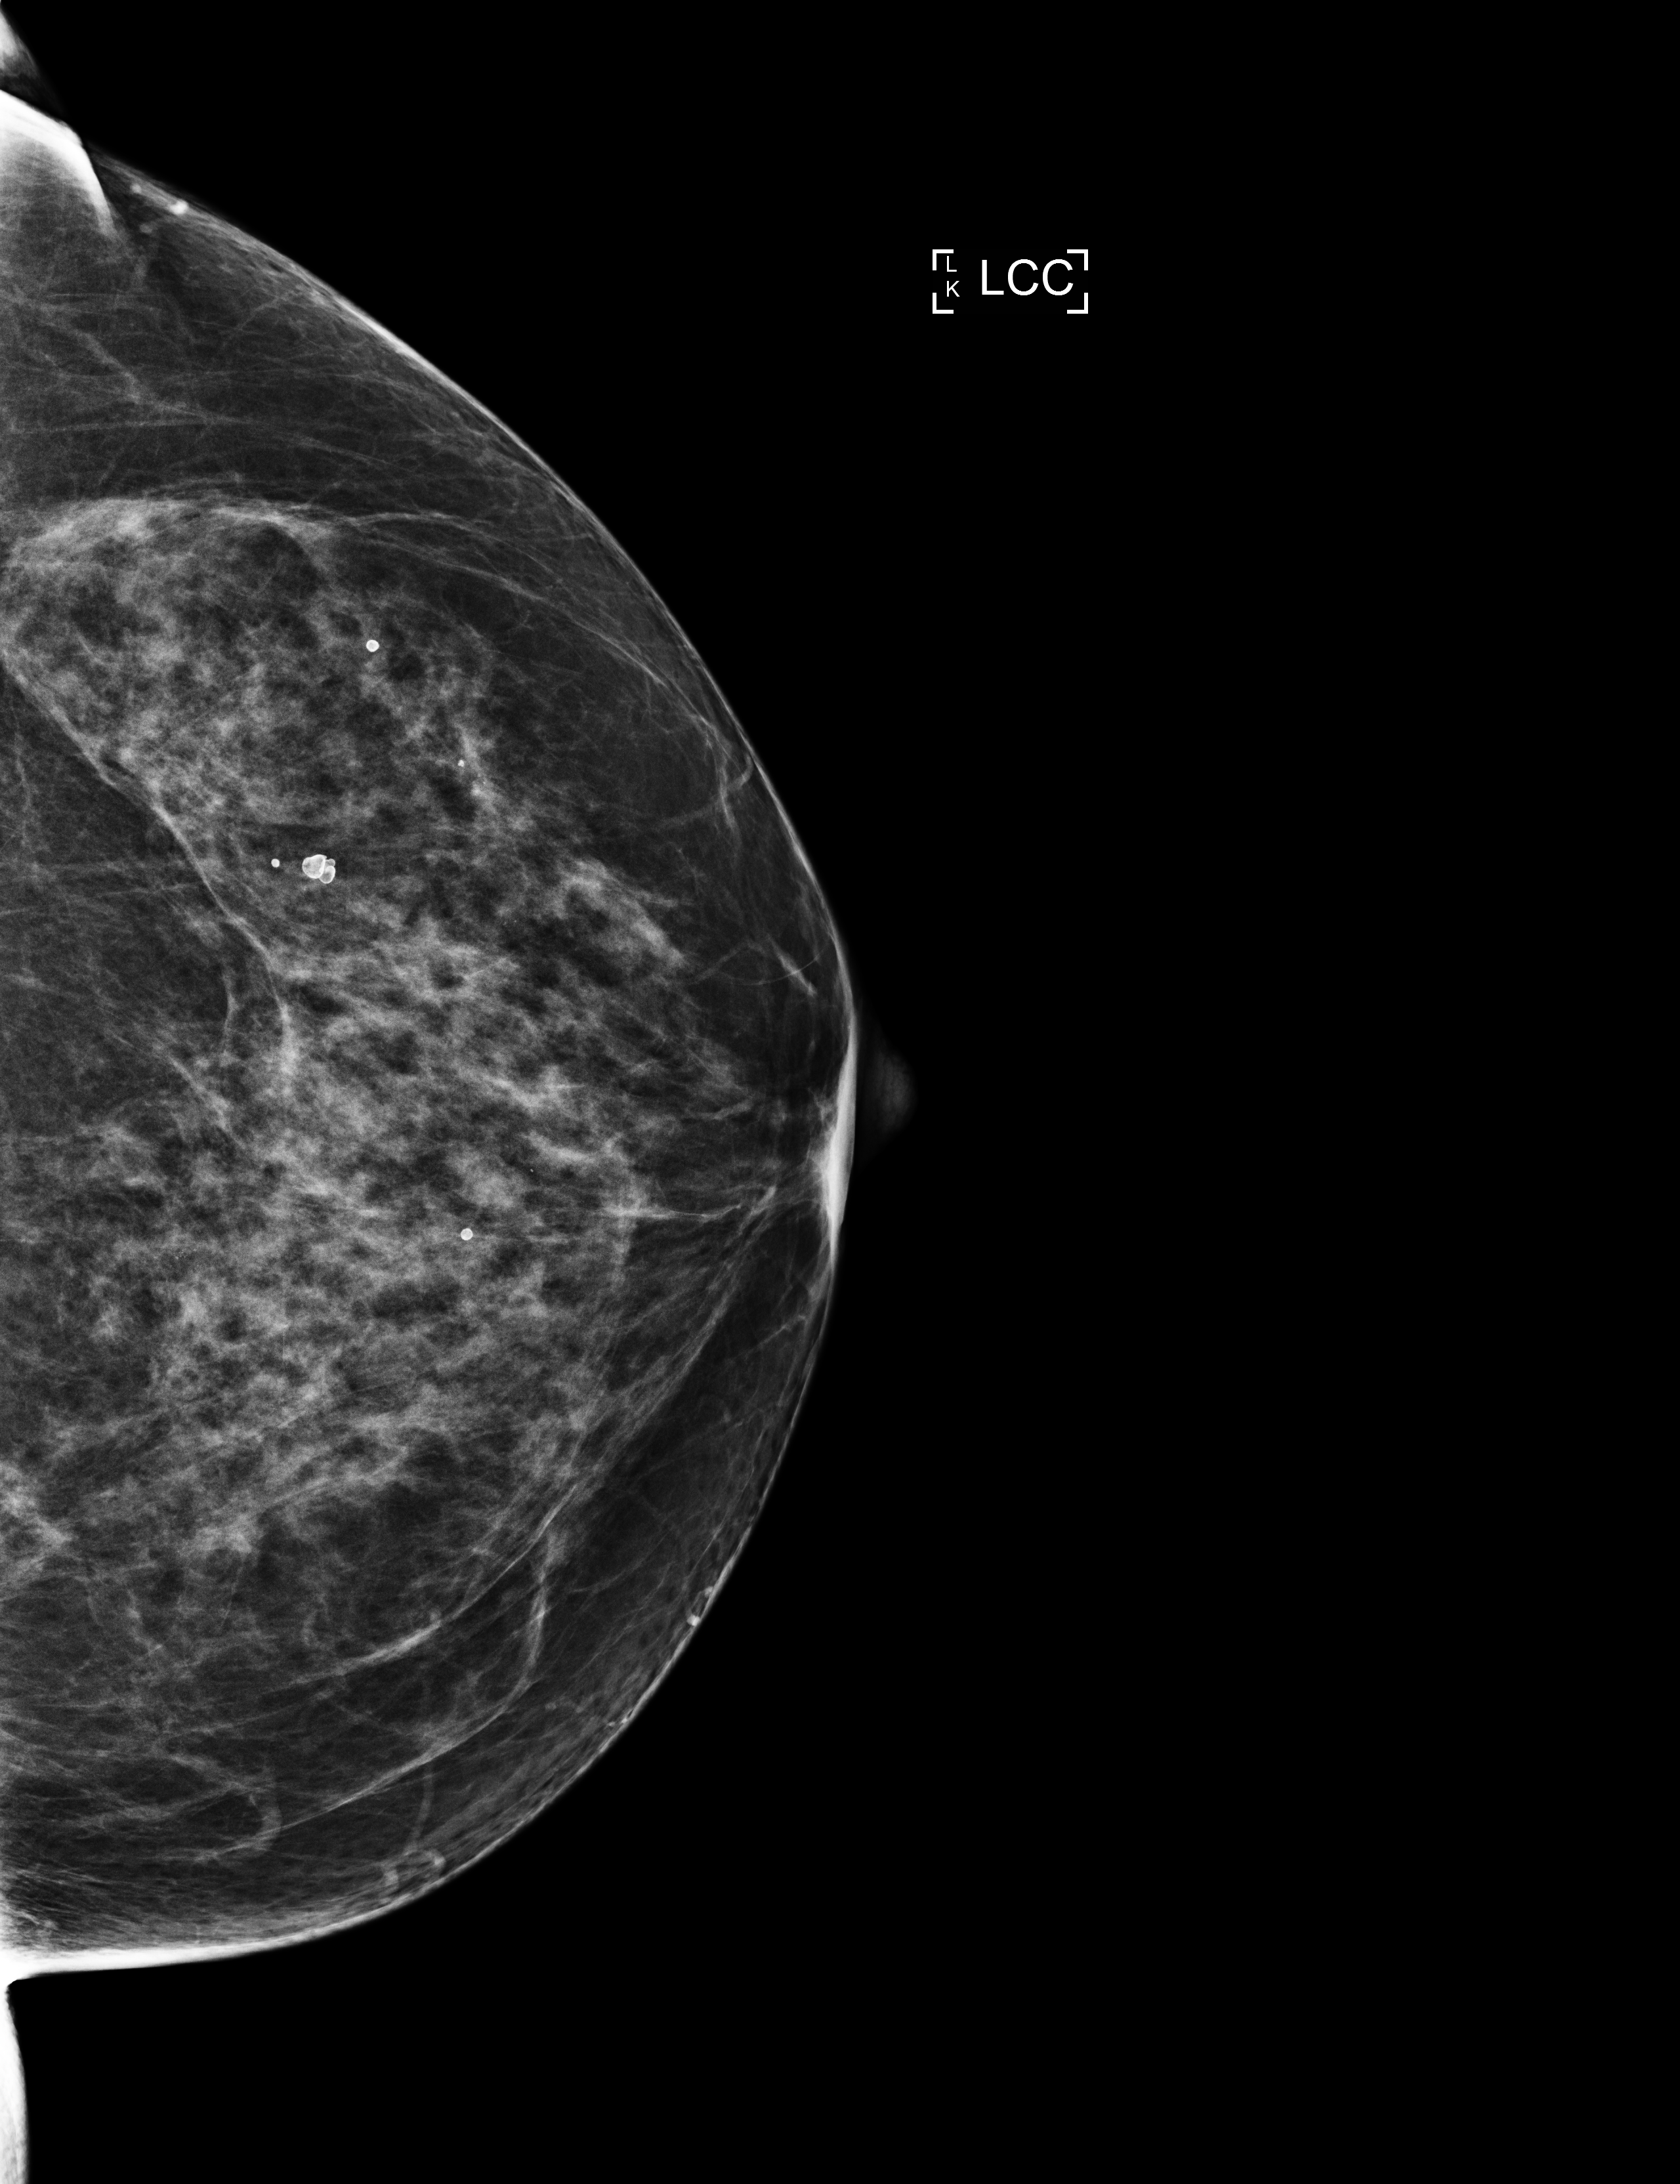
Screening examination, system: Selenia Dimensions. Patient: female, 61 years.
Image type: full-field digital mammogram. Breast: left. Projection: craniocaudal (CC) view.